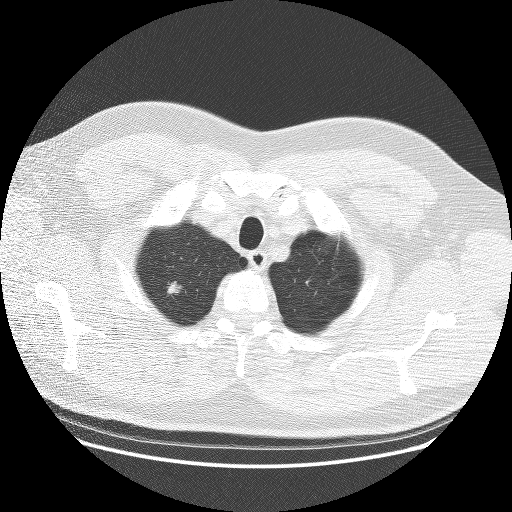
Axial slice from a low-dose chest CT screening exam; baseline screening round; lung window (W 1500 / L -600 HU); lung (sharp) reconstruction kernel (BONE); 120 kVp. Male participant, aged 65 years at enrolment.
Lesion marked by an expert reader, bounding box (x1, y1, x2, y2) in pixels: (150, 272, 194, 308). Screening reader's record for this exam (one nodule recorded; not confirmed to be the boxed lesion): non-calcified nodule or mass ≥4 mm, right upper lobe, 11 × 9 mm, poorly defined margins, soft tissue attenuation. Official screen result: positive, change unspecified: nodule(s) >= 4 mm or enlarging nodule(s), mass(es), or other non-specific abnormalities suspicious for lung cancer. Lung cancer was diagnosed 44 days after this screen: adenocarcinoma, NOS, right upper lobe, moderately differentiated (G2), stage IA (AJCC 6th edition), 11 mm at pathology.